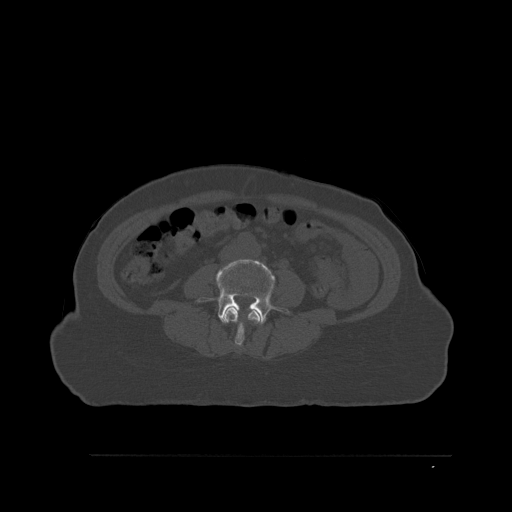
CT including the spine, one axial slice. Slice 213 of 527 in the series (ordered by position). Bone window (W 1800 / L 400 HU). 1.5 mm slice thickness. 512 × 512 image matrix, field of view 470 × 470 mm. Female patient, age 73 years. Case-level facts recorded for this patient, not image findings: primary cancer: breast.
Annotated regions visible in this slice (semi-automatic segmentation, software-assisted and operator-edited):
- L3 vertebra: bounding box (x1, y1, x2, y2) in pixels: (223, 306, 262, 347)
- L4 vertebra: (198, 258, 289, 324)